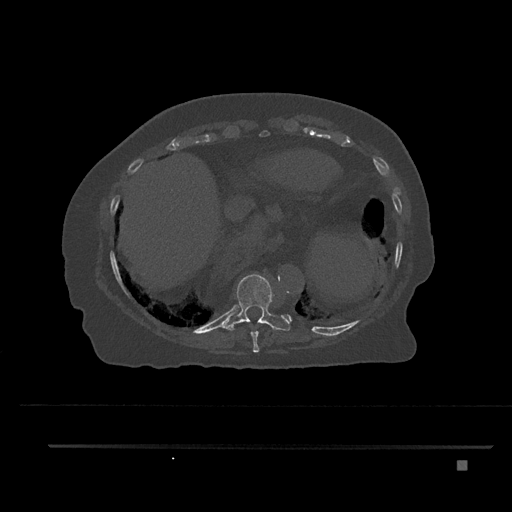
CT including the spine, one axial slice. Slice 367 of 797 in the series (ordered by position). 120 kVp. Bone window (W 1800 / L 400 HU). 512 × 512 image matrix. Patient: female, 76 years. From the clinical record (not read from this slice): primary cancer: lung.
Outlined on this slice (semi-automatically segmented with operator editing):
- T10 vertebra: bounding box [x1, y1, x2, y2] px = [220, 274, 290, 331]
- T9 vertebra: [250, 321, 260, 353]